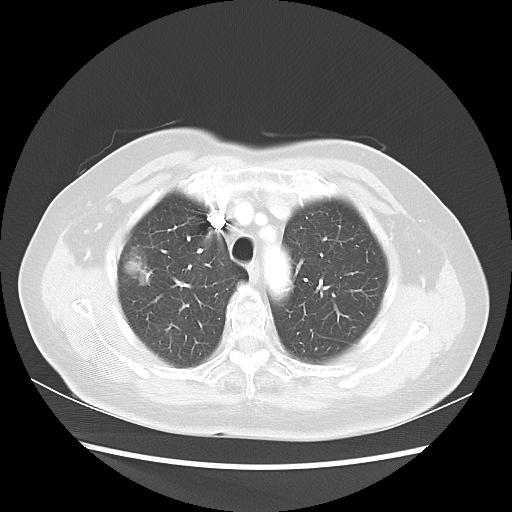
Chest CT, one axial slice; slice 37 of 48 in the series (ordered by position); 100 kVp; lung window (W 1500 / L -600 HU); 512 × 512 image matrix, field of view 360 × 360 mm. Female patient, age 75 years. Case-level facts recorded for this patient, not image findings: clinical TNM (as recorded): T1c N0 M0.
Annotated regions visible in this slice (rectangle marked by the reading radiologist):
- lung tumour (recorded histology: adenocarcinoma): box from (x=122, y=245) to (x=155, y=291) px